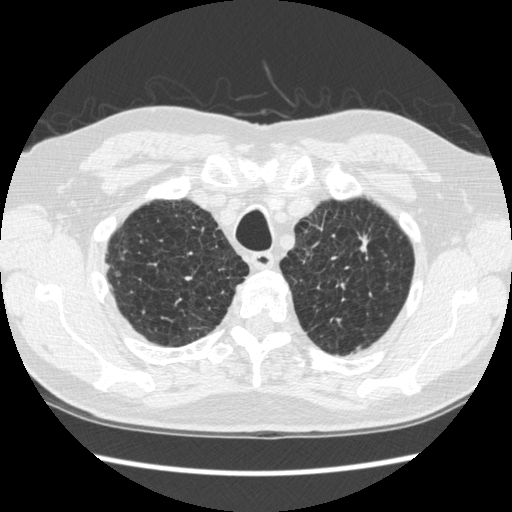
Axial slice from a low-dose chest CT screening exam, second annual screen, lung window (W 1500 / L -600 HU), 1.25 mm slice thickness, 512 × 512 image matrix, field of view 348 × 348 mm. Male participant, aged 70 years at enrolment. Former smoker at enrolment.
Expert-annotated lung lesion, box from (x=331, y=218) to (x=392, y=285) px. The screening reader recorded 5 non-calcified nodules or masses ≥4 mm on this exam (right lower lobe, right lower lobe, right lower lobe, left upper lobe, left lower lobe); which of them this box marks is not recorded. Participant outcome: lung cancer diagnosed 479 days after this screen — squamous cell carcinoma, NOS, left upper lobe, moderately differentiated (G2), stage IA (AJCC 6th edition), 18 mm at pathology.